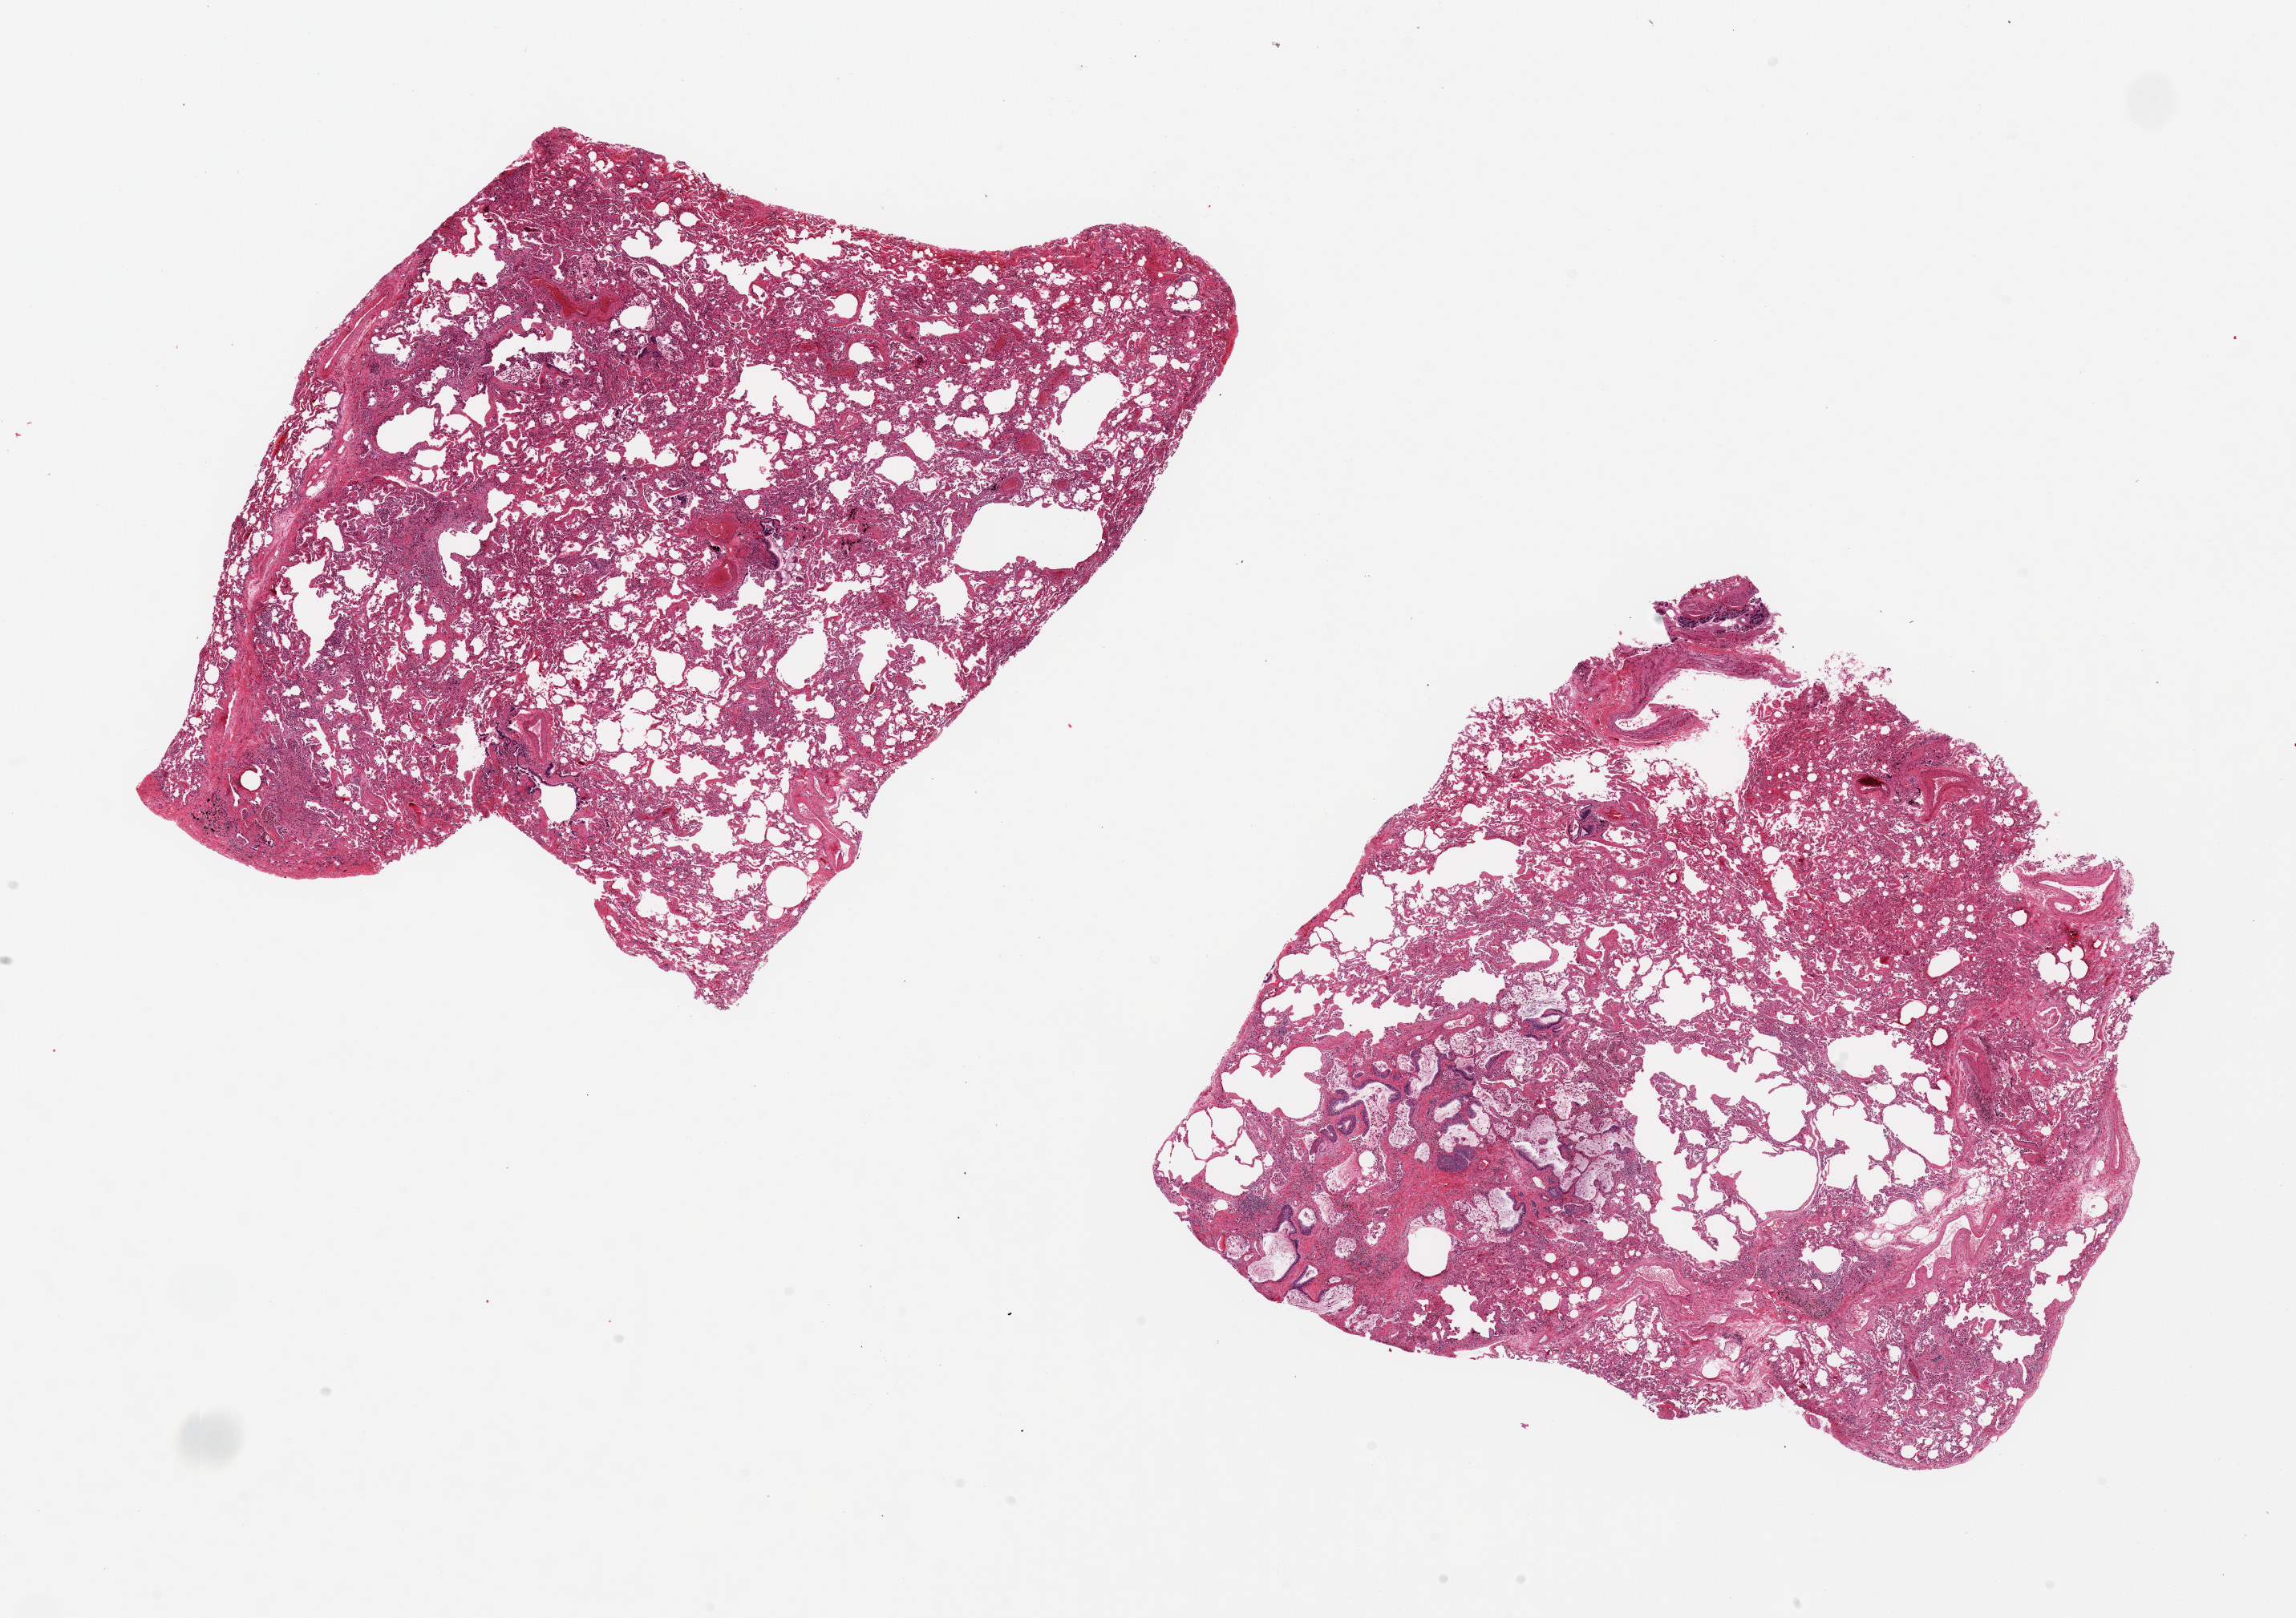
H&E whole-slide image, brightfield — low-resolution overview of the scanned area, about 22.6 x 16.0 mm; PAXgene-fixed paraffin-embedded (PFPE) section; target tissue: lung; tissue donor sample.
Pathologist's review note for this sample: 2 pieces ~8x7mm, moderate congestion.